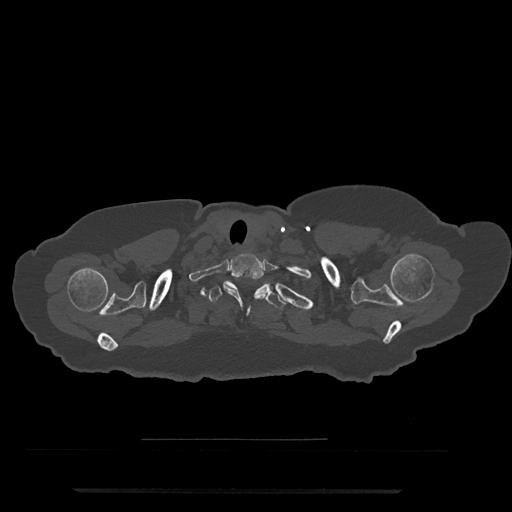
CT including the spine, one axial slice. Reconstruction kernel Br40s/3. 120 kVp. Bone window (W 1800 / L 400 HU). 512 × 512 image matrix, field of view 440 × 440 mm. Female patient, age 51 years. Case-level facts recorded for this patient, not image findings: primary cancer: neuro; vertebrae with lytic lesions (as recorded): T8.
Structures marked on this image (semi-automatically segmented with operator editing):
- T1 vertebra: bounding box [x1, y1, x2, y2] px = [223, 254, 266, 315]
- T2 vertebra: [208, 280, 286, 310]